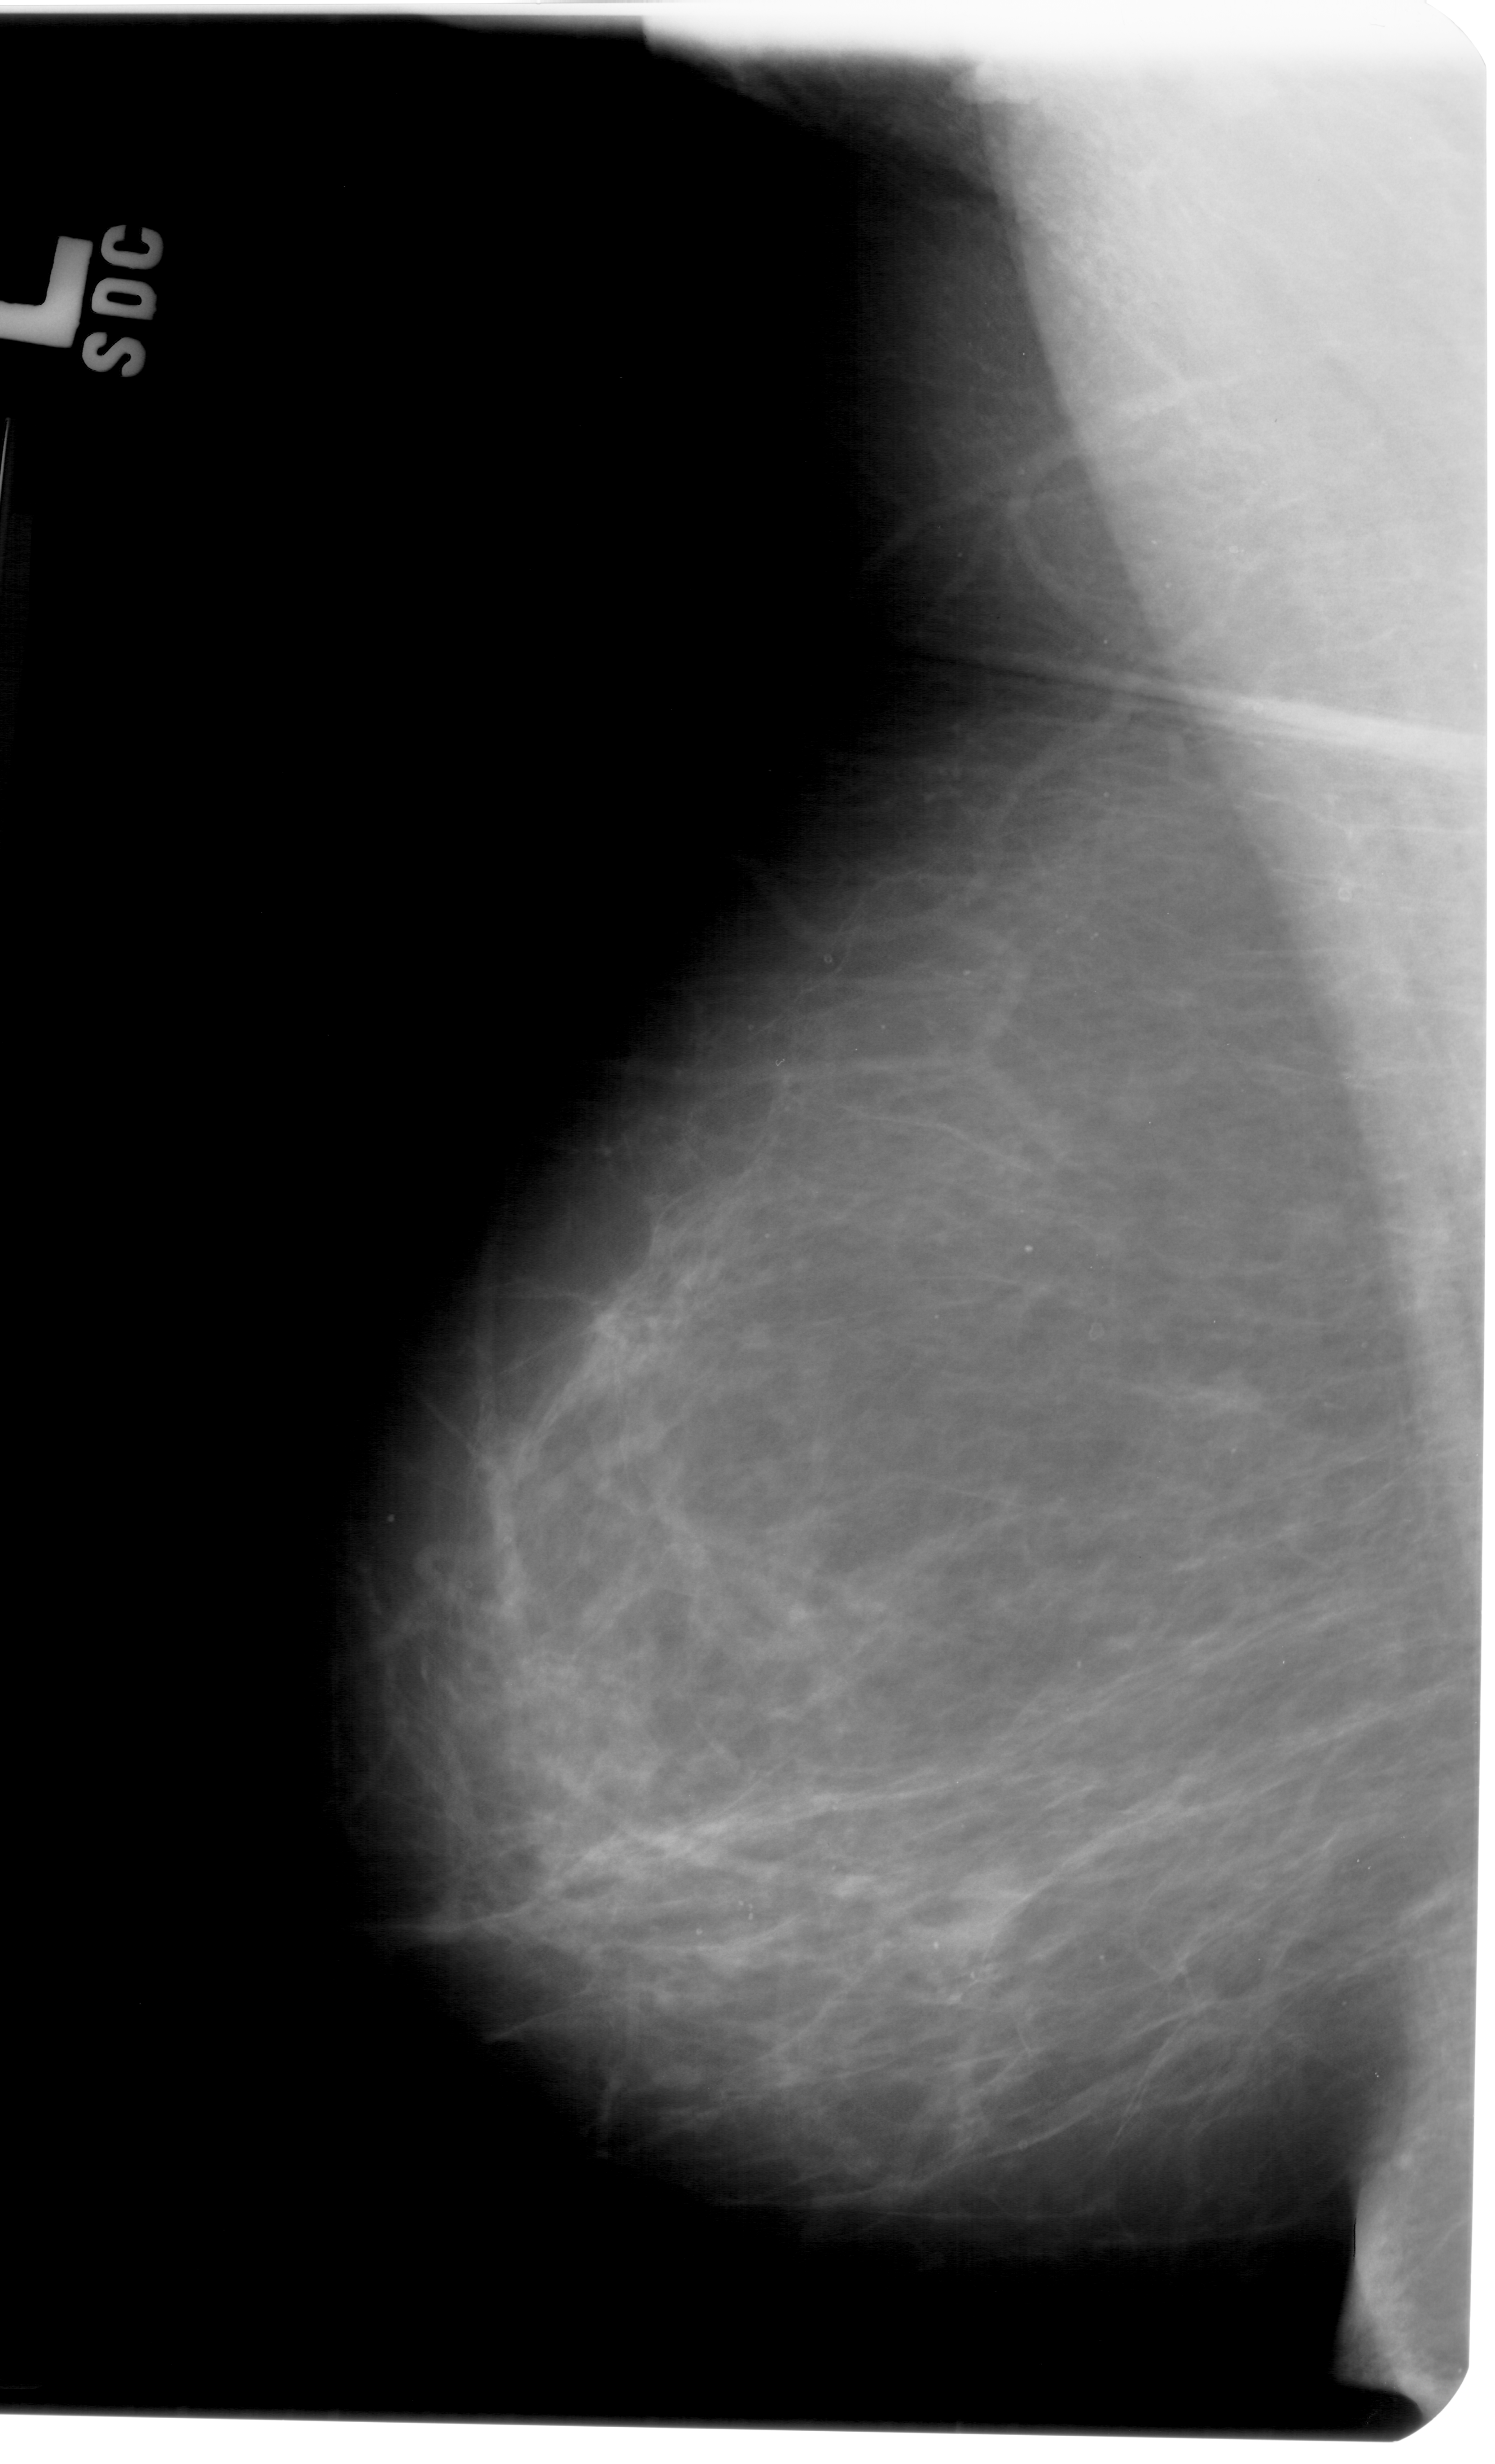
Digitized screen-film mammogram; left breast; mediolateral oblique (MLO) view; BI-RADS breast density category 3 (scale 1–4); 1495 × 2464 image matrix.
Expert-marked regions of interest on this image (one box per marked abnormality):
- mass, shape oval, margins circumscribed / obscured; BI-RADS assessment category 4; pathology result (as recorded, not read from the image): benign: bounding box <900,1859,1043,2002> (left, top, right, bottom; pixels)